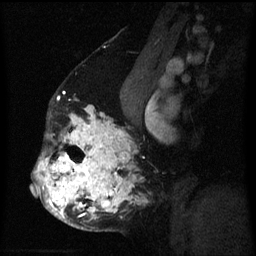
Breast MRI (dynamic contrast-enhanced), one sagittal slice. Position 37 of 60 along the scan axis. Dynamic contrast-enhanced series, image 2 of 3 at this slice position (ordered by acquisition). 1.5 T. TE 4.2 ms, TR 8 ms. 2 mm slice thickness. 256 × 256 image matrix. Patient: female, 50 years.
Structures marked on this image (semi-automatic segmentation, software-assisted and operator-edited):
- analysis volume of interest (the breast-tissue region the enhancement analysis was run in; not a lesion): bounding box (x1, y1, x2, y2) in pixels: (32, 106, 137, 231)
- tumour enhancement mask (voxels above the 70 % enhancement threshold inside the analysis volume of interest): (32, 106, 128, 219)